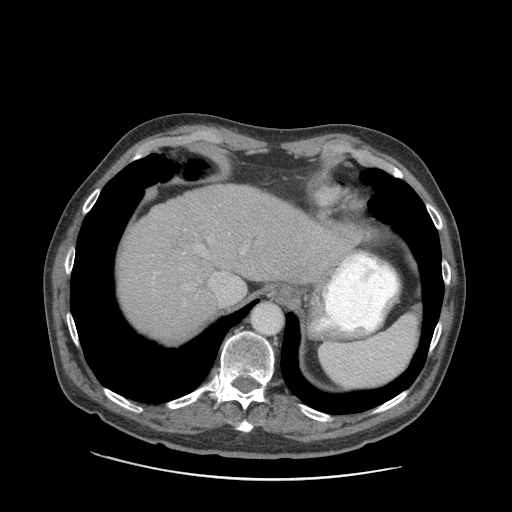
Contrast-enhanced abdominal CT (liver protocol), one axial slice. Slice 73 of 89 in the series (ordered by position). 140 kVp. Soft-tissue window (W 400 / L 40 HU). 2.5 mm slice thickness. 512 × 512 image matrix, field of view 420 × 420 mm. From the clinical record (not read from this slice): diagnosis: hepatocellular carcinoma (patient treated with transarterial chemoembolisation; whether this scan precedes or follows treatment is not stated here); TNM stage (as recorded): Stage-I; Child-Pugh class: A; tumour differentiation: moderately differentiated; tumour nodularity: uninodular.
Annotated regions visible in this slice (semi-automatically segmented with operator editing):
- liver parenchyma outside the tumour (the mass and vessels are separate outlines, so this box may not span the whole liver): box from (x=118, y=184) to (x=365, y=341) px
- liver vessels: (x=152, y=229)–(x=244, y=302)